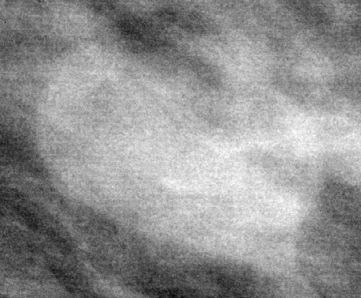
Region of interest cut from a scanned film mammogram (one marked finding), left breast, MLO view.
Mass, shape oval, margins circumscribed; BI-RADS assessment category 3; pathology result (as recorded, not read from the image): benign.